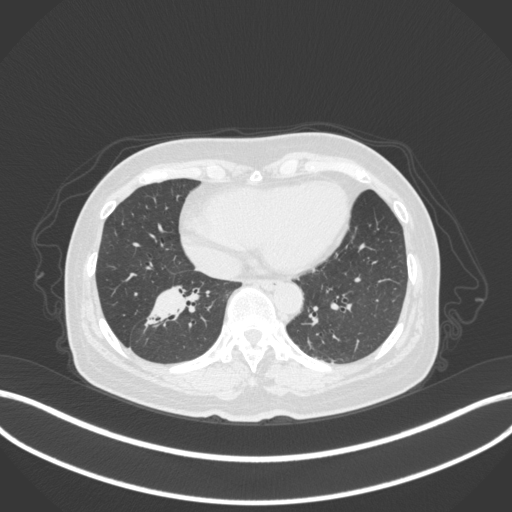
Chest CT, one axial slice. Lung window (W 1500 / L -600 HU). 1 mm slice thickness. 512 × 512 image matrix, field of view 400 × 400 mm. Patient: female, 67 years. From the clinical record (not read from this slice): clinical TNM (as recorded): T1c N1 M0; histopathological grade: G2-3.
Structures marked on this image (bounding box drawn by a radiologist):
- lung tumour (recorded histology: adenocarcinoma): bounding box (x1, y1, x2, y2) in pixels: (139, 279, 205, 337)